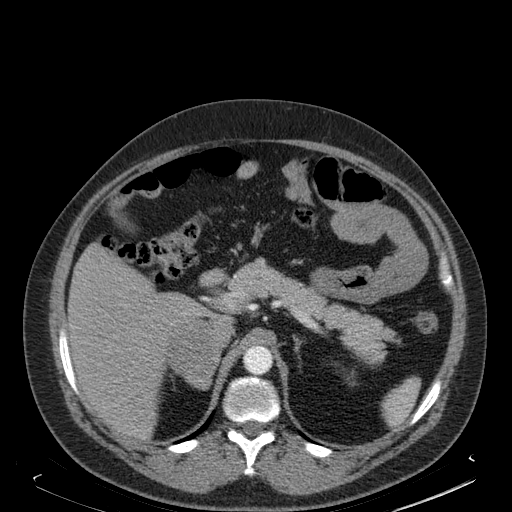
Contrast-enhanced abdominal CT, one axial slice. Slice 118 of 181 in the series (ordered by position). Soft-tissue window (W 400 / L 40 HU). 1.5 mm slice thickness. 512 × 512 image matrix, field of view 405 × 405 mm. Male patient. From the clinical record (not read from this slice): diagnosis: adrenocortical carcinoma; tumour side: right adrenal; tumour size at pathology: 7.5 cm; Ki-67 index: 25 %; stage (as recorded): 4.
Annotated regions visible in this slice (semi-automatic segmentation, software-assisted and operator-edited):
- mass: box from (x=168, y=319) to (x=219, y=389) px